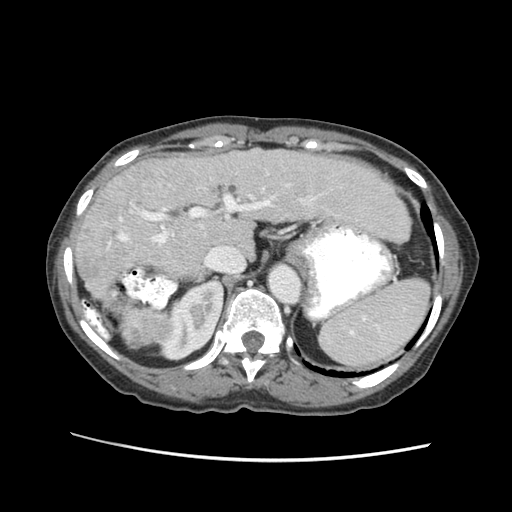
Contrast-enhanced abdominal CT (liver protocol), one axial slice. Position 40 of 63 along the scan axis. 120 kVp. Soft-tissue window (W 400 / L 40 HU). 2.5 mm slice thickness. 512 × 512 image matrix. Case-level facts recorded for this patient, not image findings: diagnosis: hepatocellular carcinoma (patient treated with transarterial chemoembolisation; whether this scan precedes or follows treatment is not stated here); TNM stage (as recorded): Stage-I; Child-Pugh class: B; tumour differentiation: well differentiated; tumour nodularity: uninodular.
Annotated regions visible in this slice (semi-automatic segmentation, software-assisted and operator-edited):
- liver parenchyma outside the tumour (the mass and vessels are separate outlines, so this box may not span the whole liver): bounding box <74,146,410,323> (left, top, right, bottom; pixels)
- mass: <118,306,174,351>
- liver vessels: <119,186,322,245>